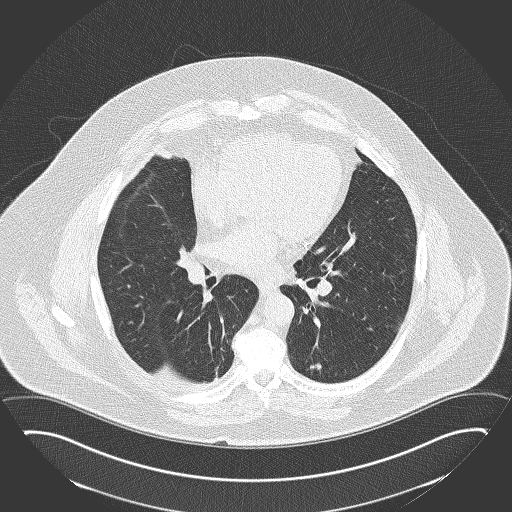
Low-dose screening chest CT, axial slice, second screening round (one year after baseline), lung window (W 1500 / L -600 HU), 2 mm slice thickness. Male participant, aged 63 years at enrolment.
Expert reader's lesion annotation, bounding box [x1, y1, x2, y2] px = [292, 349, 337, 388]. The exam's reader record, not a measurement of the box and not confirmed to be the same lesion: non-calcified nodule or mass ≥4 mm, left lower lobe, 12 × 12 mm, poorly defined margins, ground glass attenuation, pre-existing on the prior screen: no. Participant outcome: lung cancer diagnosed 550 days after this screen — squamous cell carcinoma, NOS, left lower lobe, moderately differentiated (G2), stage IA (AJCC 6th edition), 15 mm at pathology.